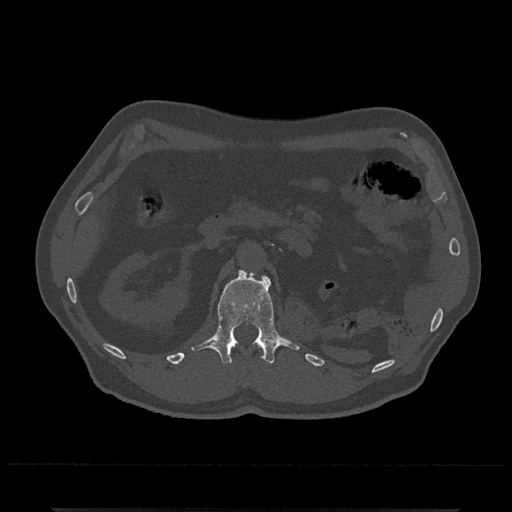
CT including the spine, one axial slice. Slice 371 of 797 in the series (ordered by position). Reconstruction kernel Br40s/3. 120 kVp. Bone window (W 1800 / L 400 HU). 0.5 mm slice thickness. 512 × 512 image matrix, field of view 393 × 393 mm. Patient: male, 67 years. Case-level facts recorded for this patient, not image findings: primary cancer: prostate.
Outlined on this slice (semi-automatically segmented with operator editing):
- L1 vertebra: bounding box (x1, y1, x2, y2) in pixels: (191, 269, 300, 365)
- T12 vertebra: (259, 345, 264, 357)